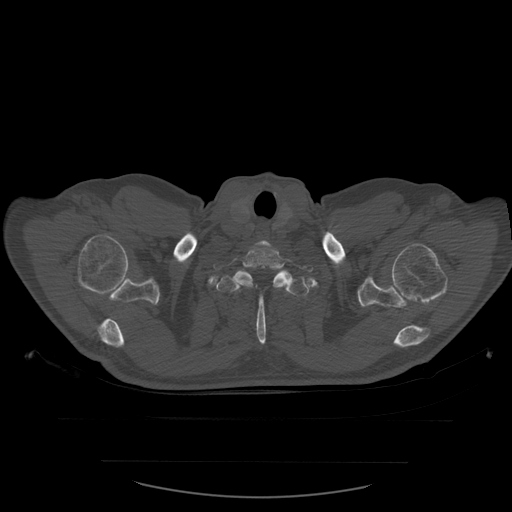
CT including the spine, one axial slice; slice 483 of 590 in the series (ordered by position); bone window (W 1800 / L 400 HU); 1.25 mm slice thickness; 512 × 512 image matrix, field of view 479 × 479 mm. Patient age 71 years. Case-level facts recorded for this patient, not image findings: primary cancer: lung; vertebrae with lytic lesions (as recorded): T1, T2, L5, S1.
Structures marked on this image (semi-automatic segmentation, software-assisted and operator-edited):
- T1 vertebra: bounding box <213,246,314,289> (left, top, right, bottom; pixels)
- T2 vertebra: <216,270,313,345>